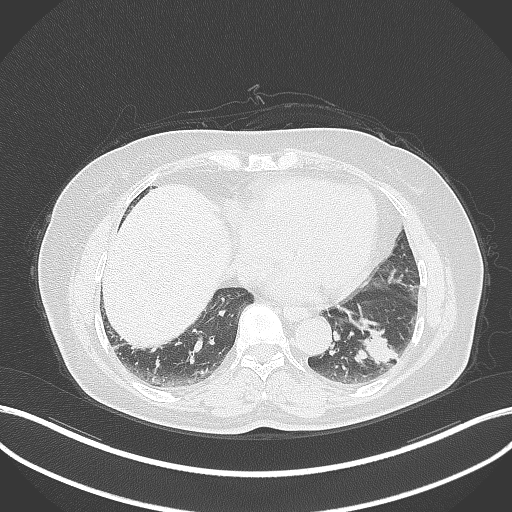
Chest CT, one axial slice. Slice 124 of 311 in the series (ordered by position). 120 kVp. Lung window (W 1500 / L -600 HU). 512 × 512 image matrix, field of view 400 × 400 mm. Patient: female, 59 years. From the clinical record (not read from this slice): clinical TNM (as recorded): T2a N0 M0; histopathological grade: G2-3.
Structures marked on this image (bounding box drawn by a radiologist):
- lung tumour (recorded histology: adenocarcinoma): bounding box (x1, y1, x2, y2) in pixels: (352, 325, 394, 370)